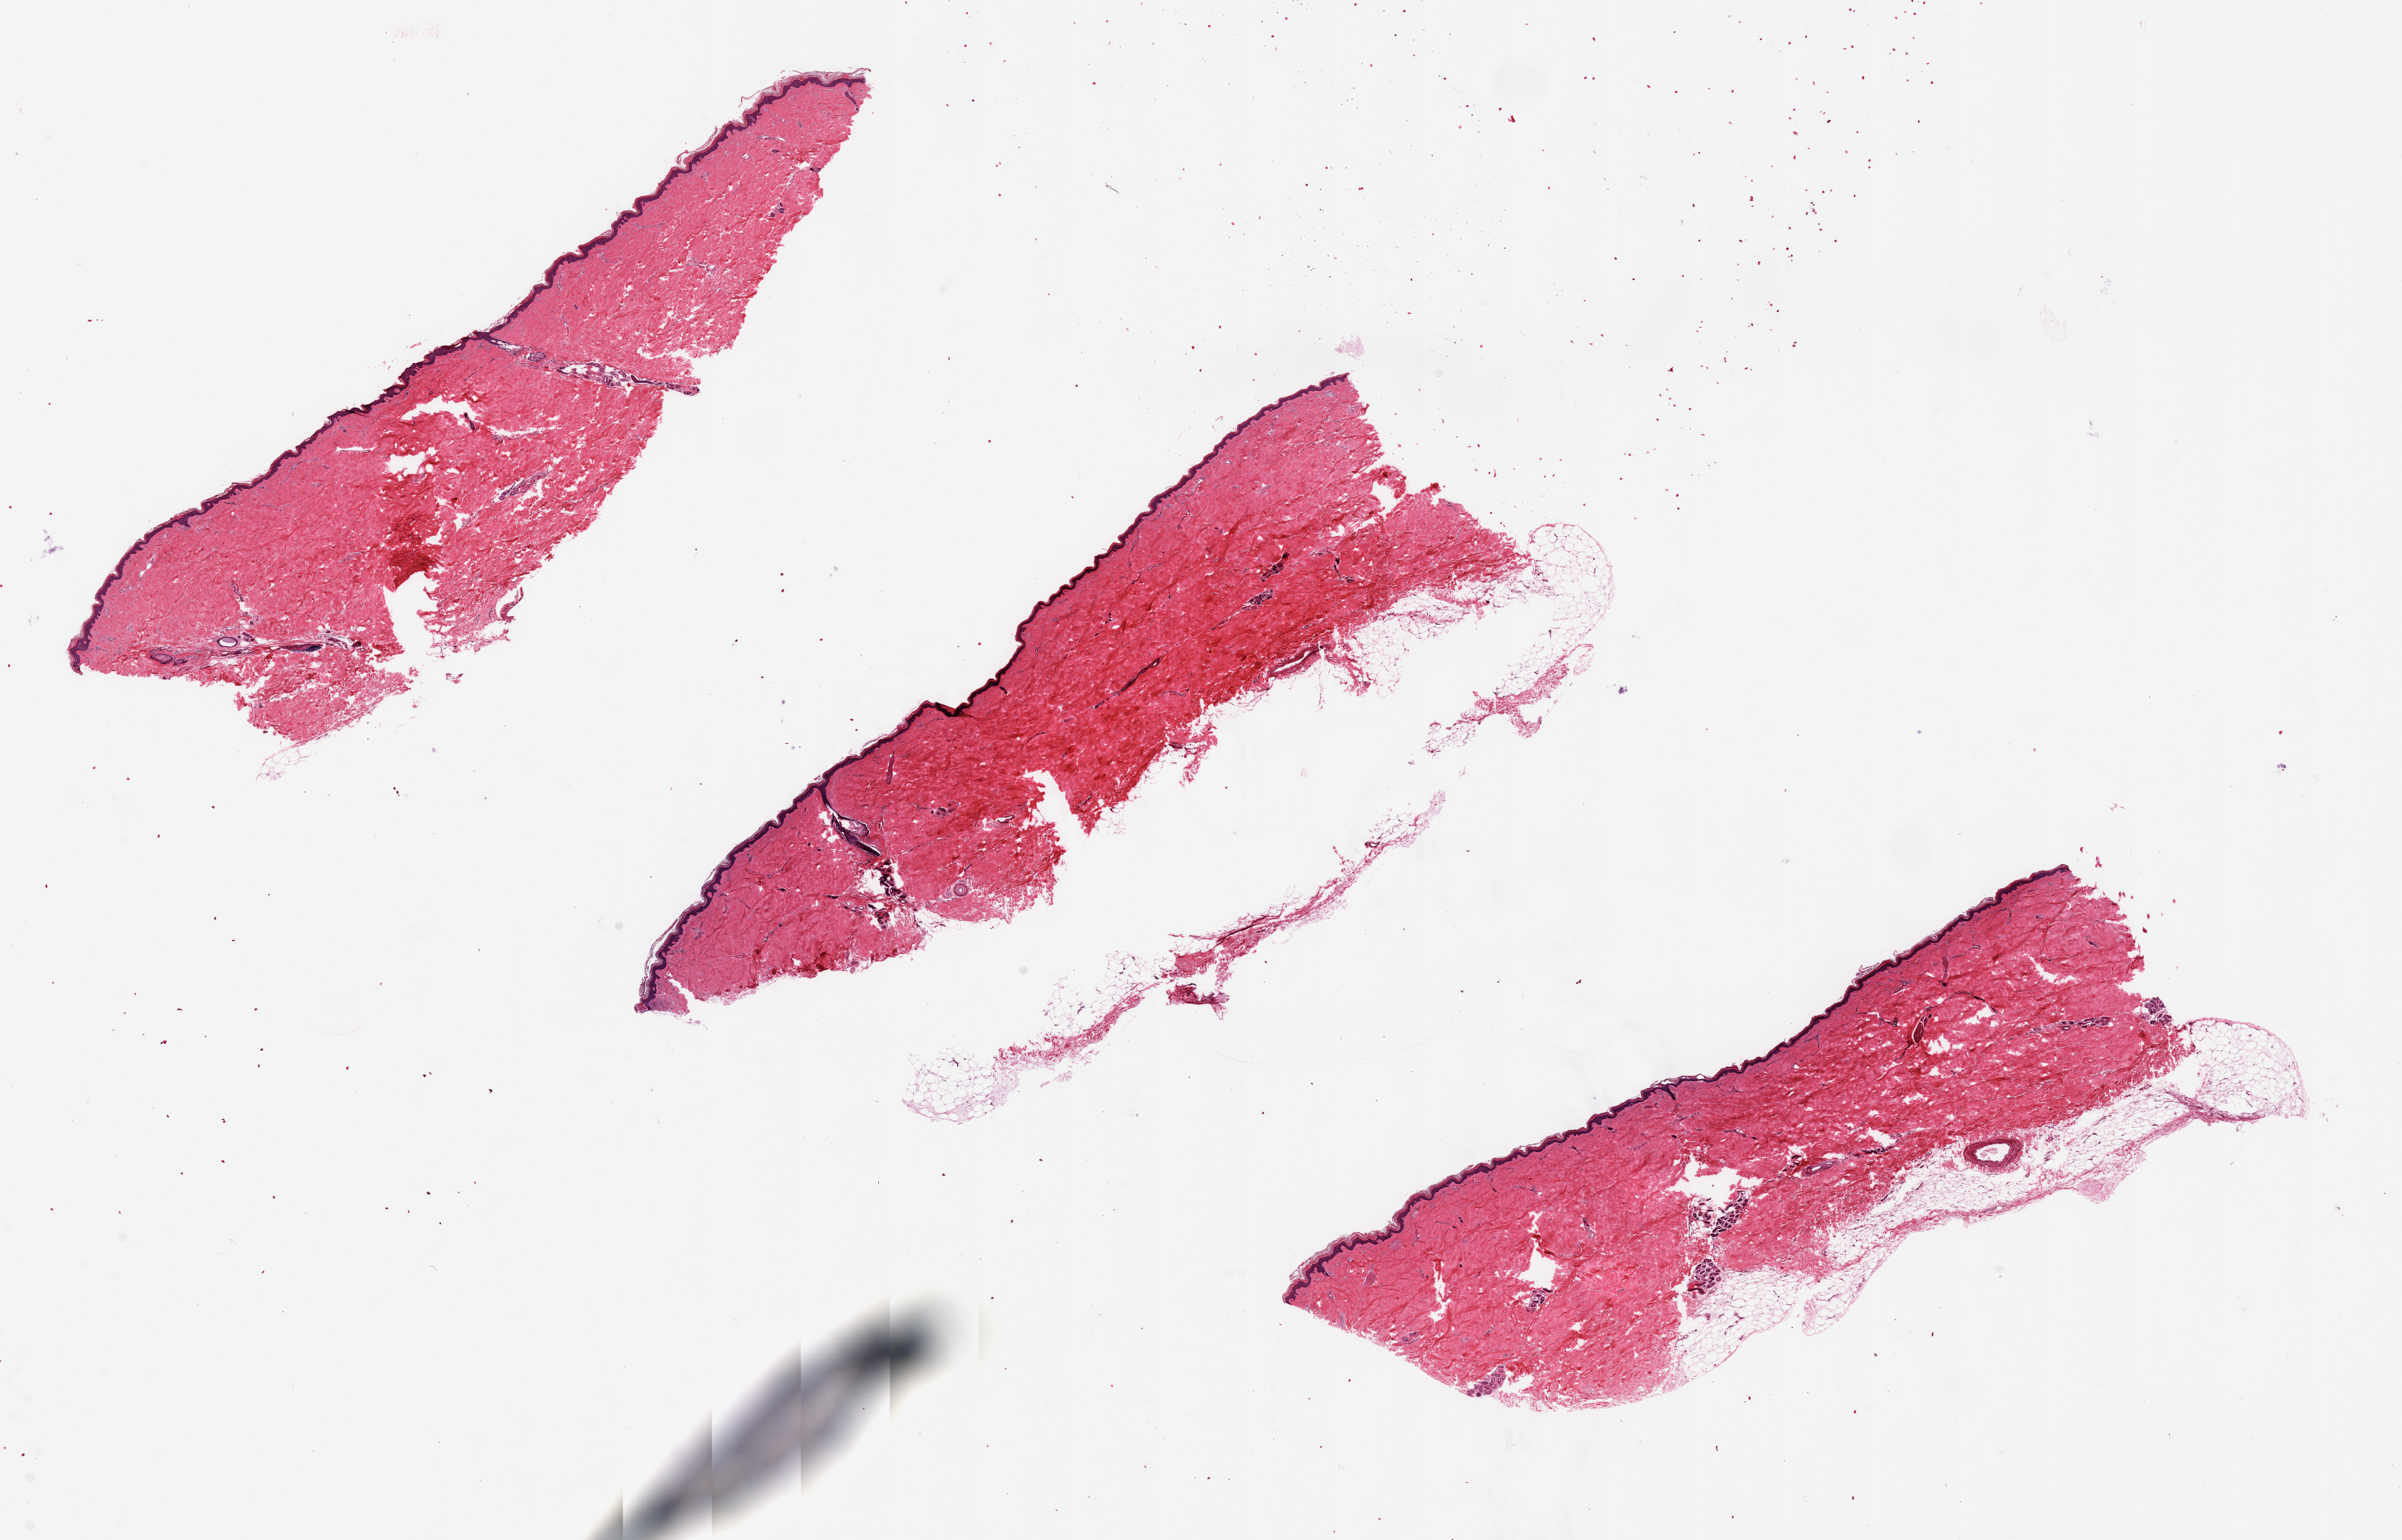
Digitized H&E-stained section — shown as a low-resolution overview of the whole scanned area (about 26.6 x 17.0 mm, acquisition: 20x scan). PAXgene-fixed paraffin-embedded (PFPE) section. Sampled site (target tissue): skin of lower leg. Donor tissue sample. Donor: male.
* pathologist's review note for this sample: Epidermis is about 2% of total thickness of specimen; mainly dermis + subcutaneous fat